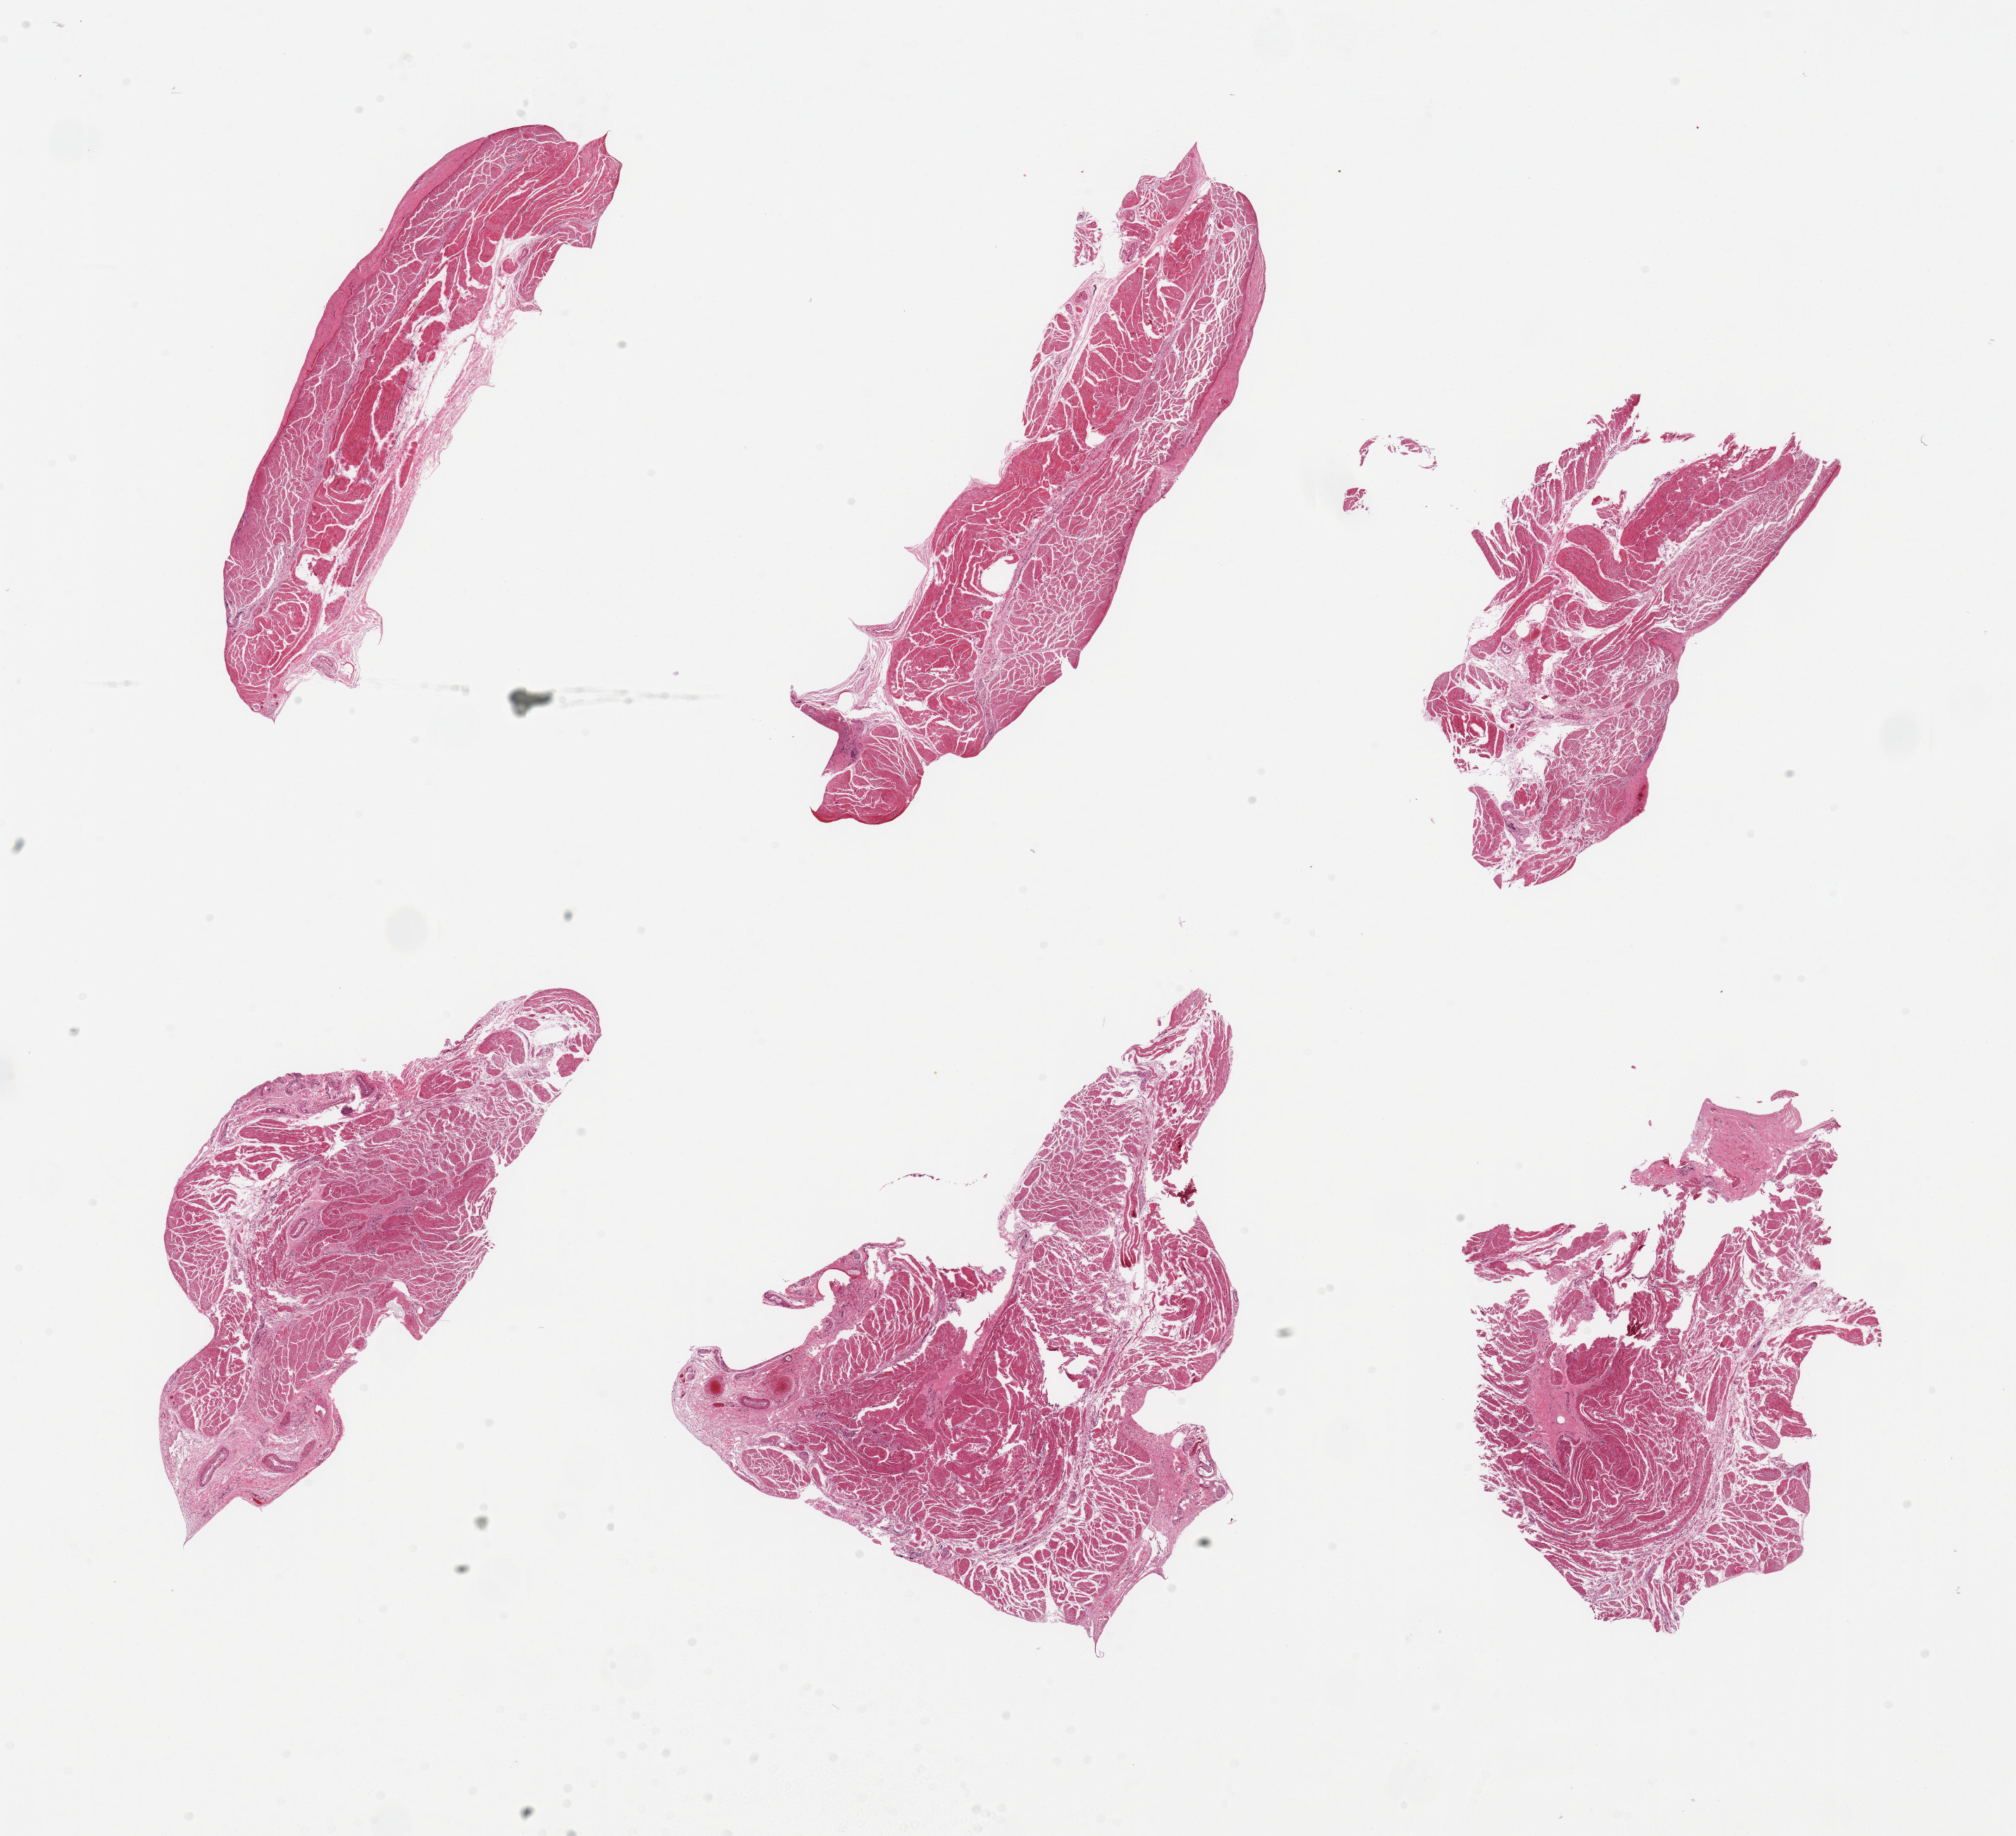
Whole-slide image, haematoxylin and eosin stain, shown as a low-resolution overview of the whole scanned area (about 22.6 x 20.6 mm, from a 20x scan); PAXgene-fixed paraffin-embedded (PFPE) section; section of esophageal muscle (target tissue); donor tissue sample. Donor sex: female.
Pathologist's review note for this sample: 6 pieces, confirmed target muscularis.